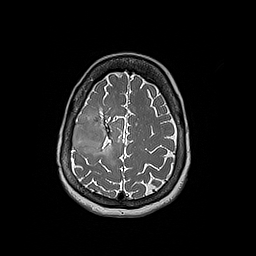
Brain MRI from a brain-tumour surgery series, one axial slice. Position 56 of 192 along the scan axis. 1 mm slice thickness. 256 × 256 image matrix. From the clinical record (not read from this slice): histopathology: Oligodendroglioma; WHO grade: 3; IDH mutation: yes; tumour location: Right Frontal.
Outlined on this slice (expert manual segmentation):
- tumour: bounding box [x1, y1, x2, y2] px = [72, 114, 105, 153]